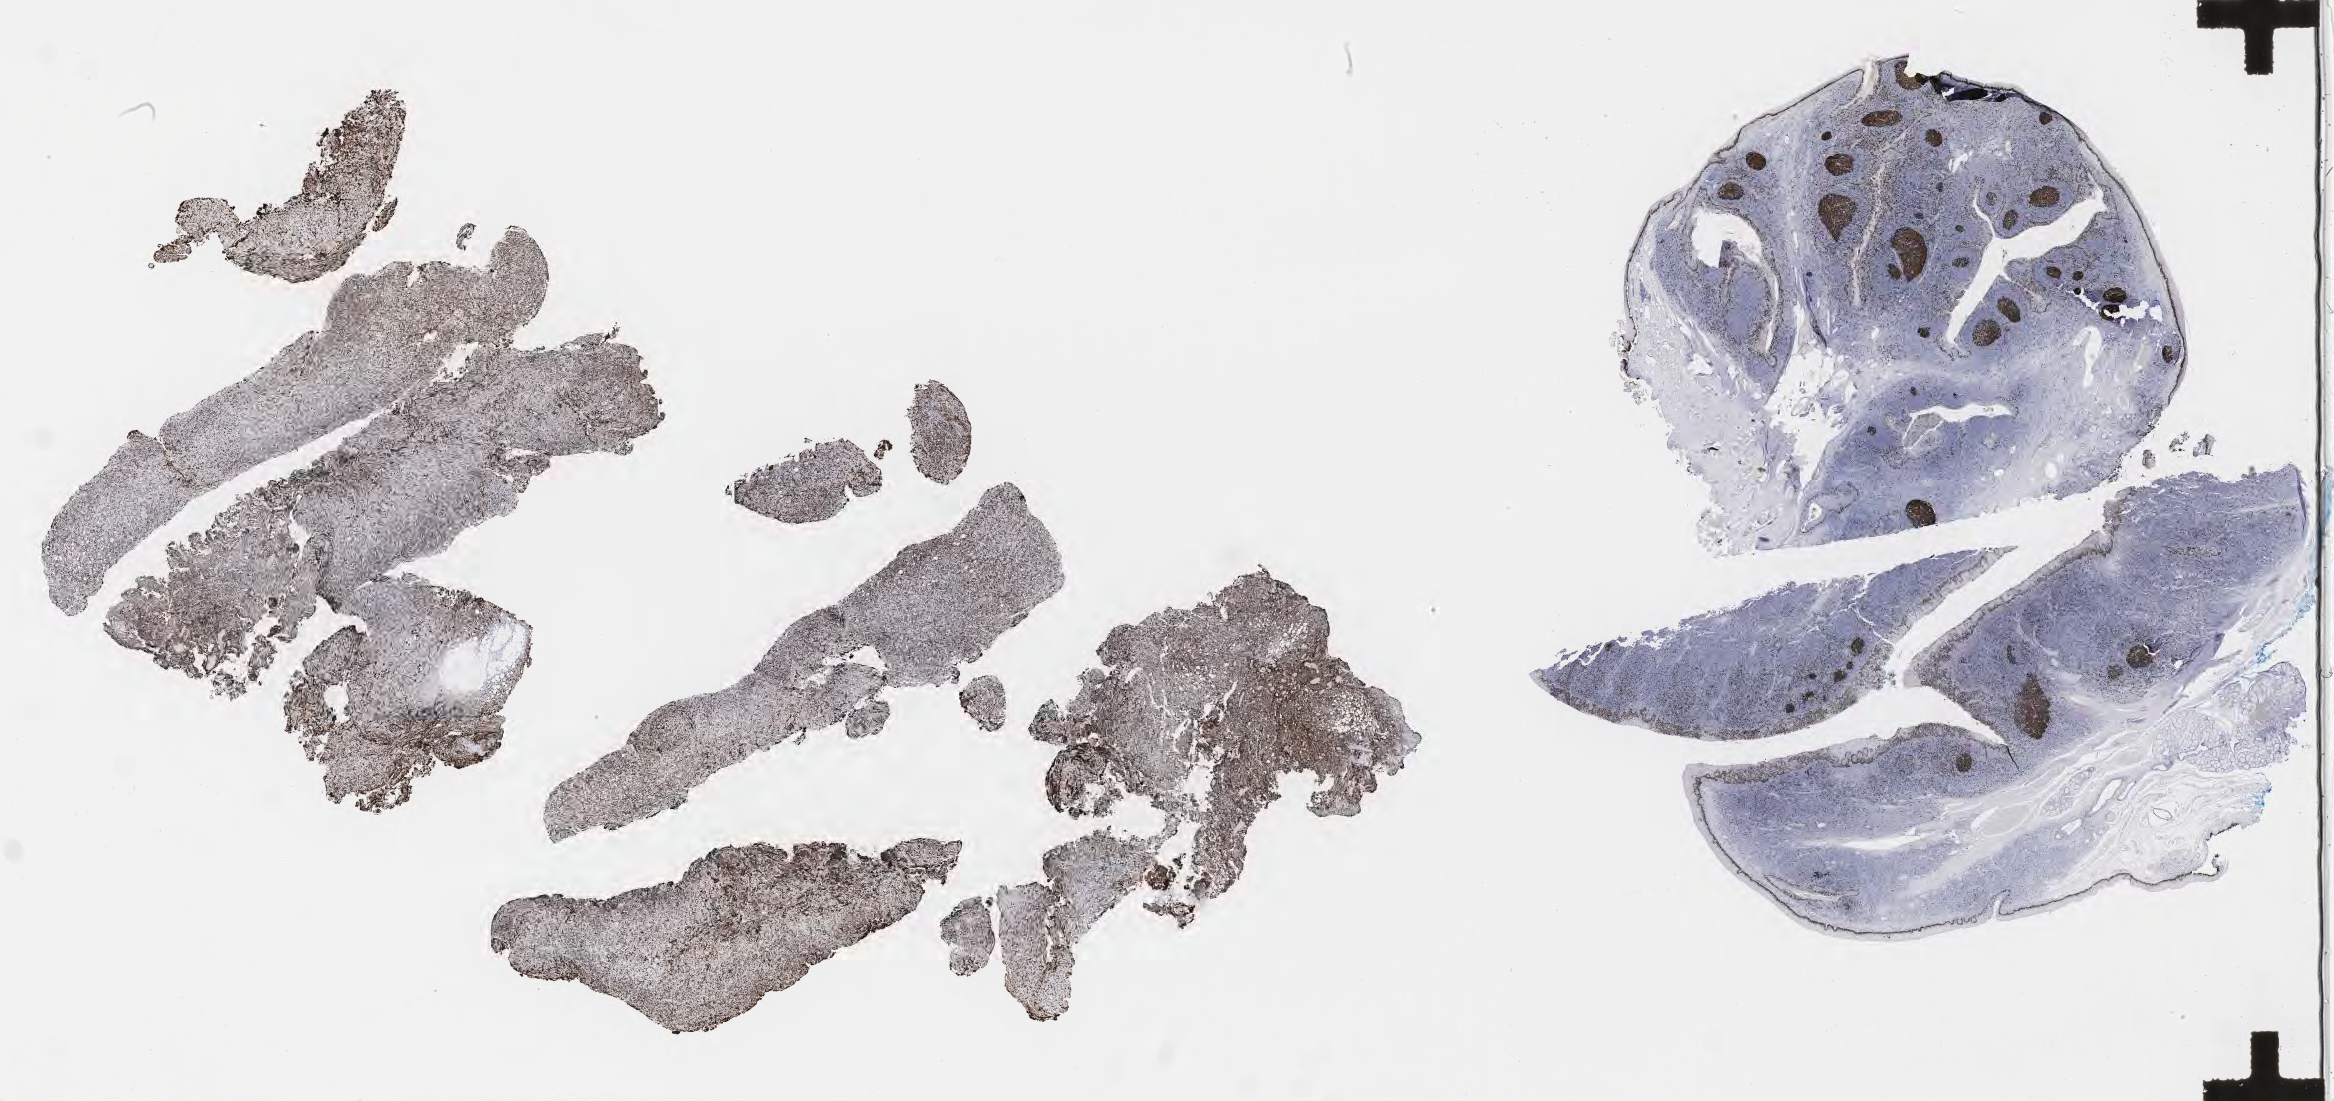
Whole-slide image, immunohistochemical stain for Ki-67, shown as a low-resolution overview of the whole scanned area (about 37.7 x 17.8 mm), tumor tissue. Male patient, aged 45.
* histologic diagnosis: Diffuse large B-cell lymphoma, NOS